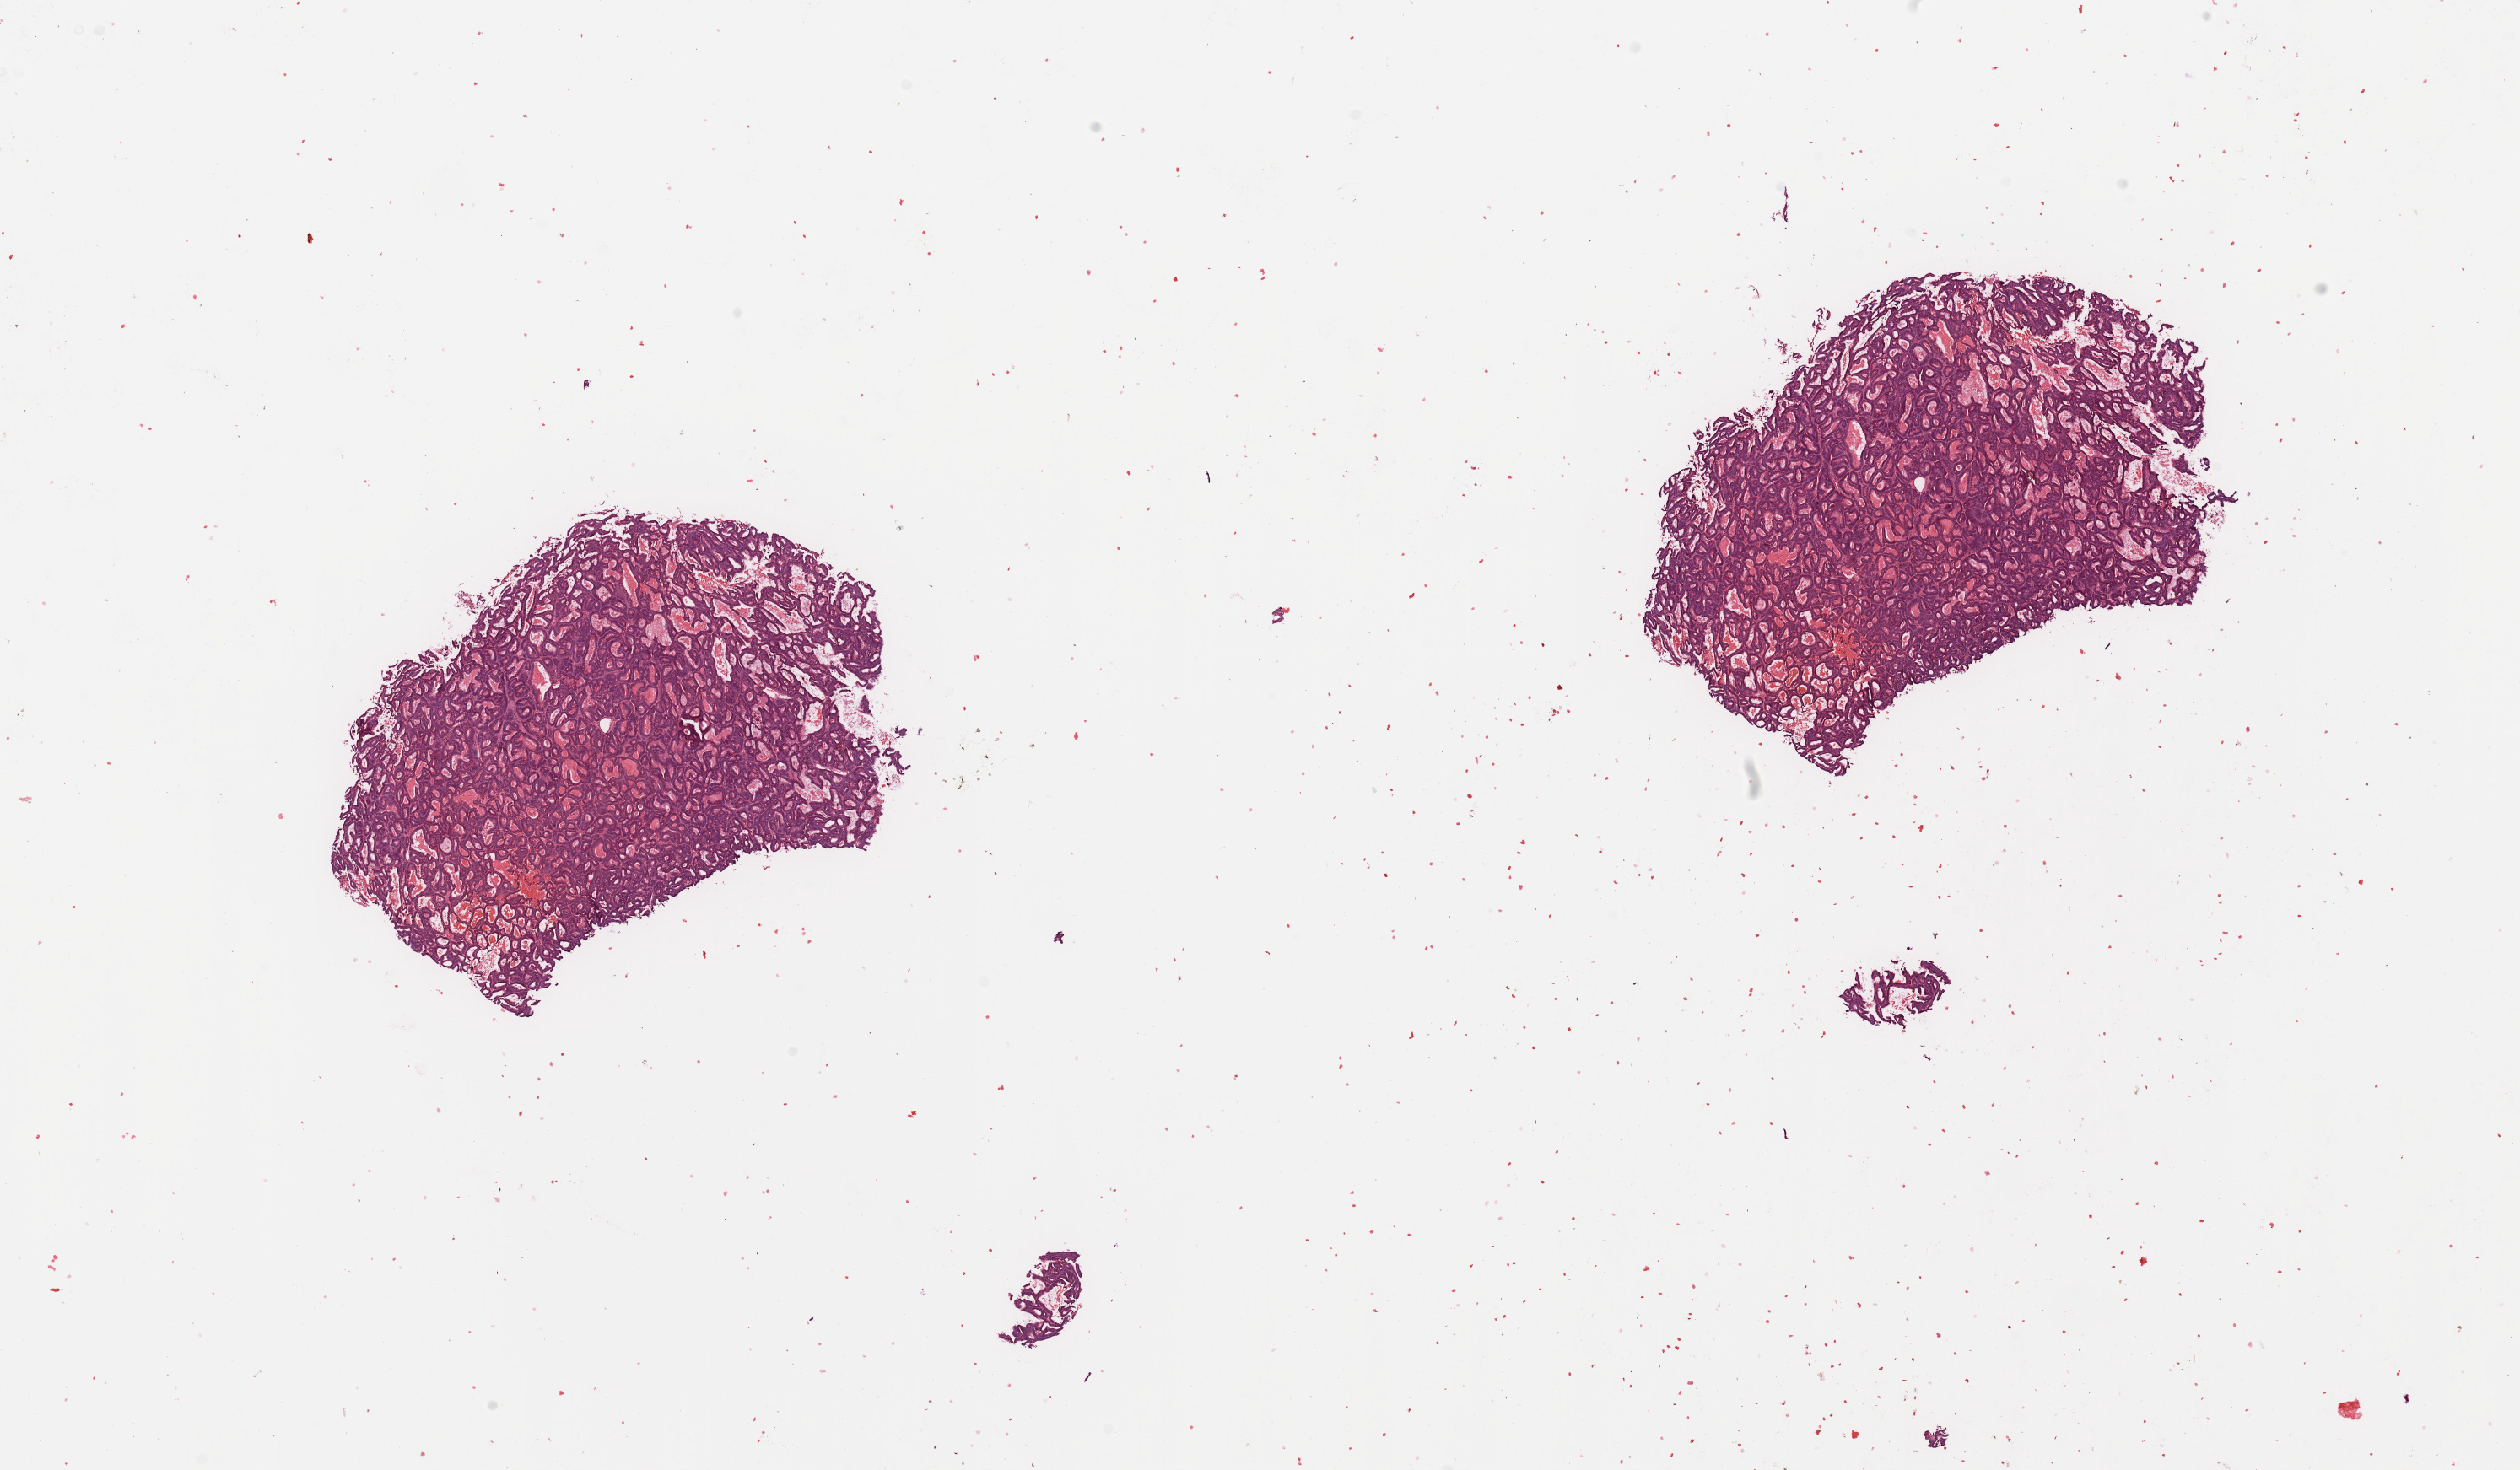
H&E whole-slide image, whole scanned area (about 23.6 x 13.8 mm, from a 20x scan) shown as a low-resolution overview; tumour tissue sample, sampled site: uterus. Female, 84 y/o. Histologic grade: G1 (well differentiated). Composition of this section per pathologist review: tumour nuclei 90%, necrosis 0%.
- primary tumour site (as recorded): anterior endometrium
- AJCC pathologic stage: I
- histologic diagnosis: Endometrioid adenocarcinoma, NOS